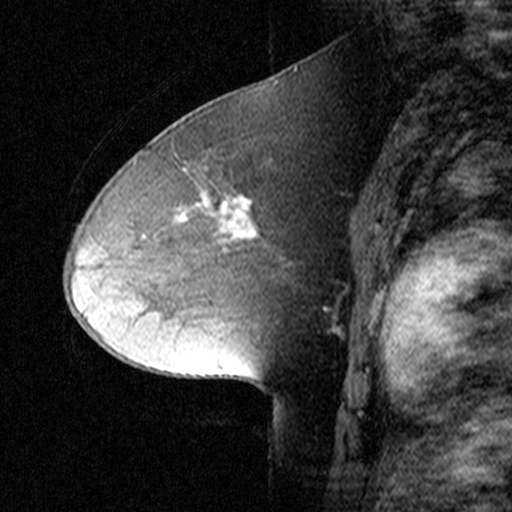
Breast MRI (dynamic contrast-enhanced), one sagittal slice; slice 22 of 44 in the series (ordered by position); dynamic contrast-enhanced study with each time point stored as its own series, time point 2 of 3 at this slice position (early post-contrast, ordered by acquisition time); 1.5 T; TE 4.5 ms, TR 11 ms; 3 mm slice thickness; 512 × 512 image matrix, field of view 200 × 200 mm. Female patient, age 50 years. From the clinical record (not read from this slice): setting: breast cancer imaged before/during neoadjuvant chemotherapy; receptor status: HR-positive, HER2-negative.
Structures marked on this image (semi-automatically segmented with operator editing):
- analysis volume of interest (the breast-tissue region the enhancement analysis was run in; not a lesion): bounding box (x1, y1, x2, y2) in pixels: (154, 164, 313, 287)
- tumour enhancement mask (voxels above the 90 % enhancement threshold inside the analysis volume of interest): (206, 195, 254, 236)